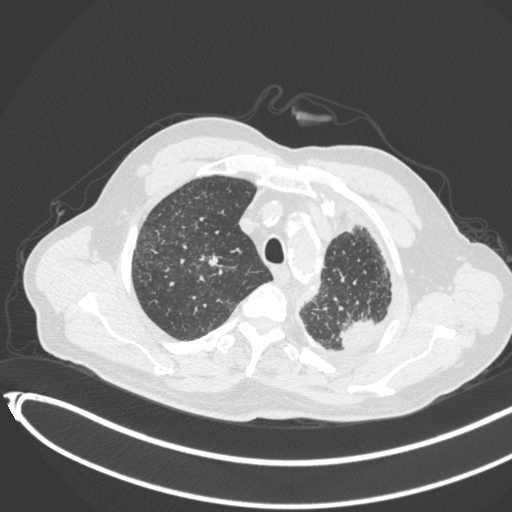
Chest CT, one axial slice. Slice 352 of 451 in the series (ordered by position). 120 kVp. Lung window (W 1500 / L -600 HU). 1 mm slice thickness. 512 × 512 image matrix, field of view 400 × 400 mm. Patient: male, 78 years. Case-level facts recorded for this patient, not image findings: clinical TNM (as recorded): T1c N0 M1.
Outlined on this slice (bounding box drawn by a radiologist):
- lung tumour (recorded histology: adenocarcinoma): bounding box <334,314,383,355> (left, top, right, bottom; pixels)